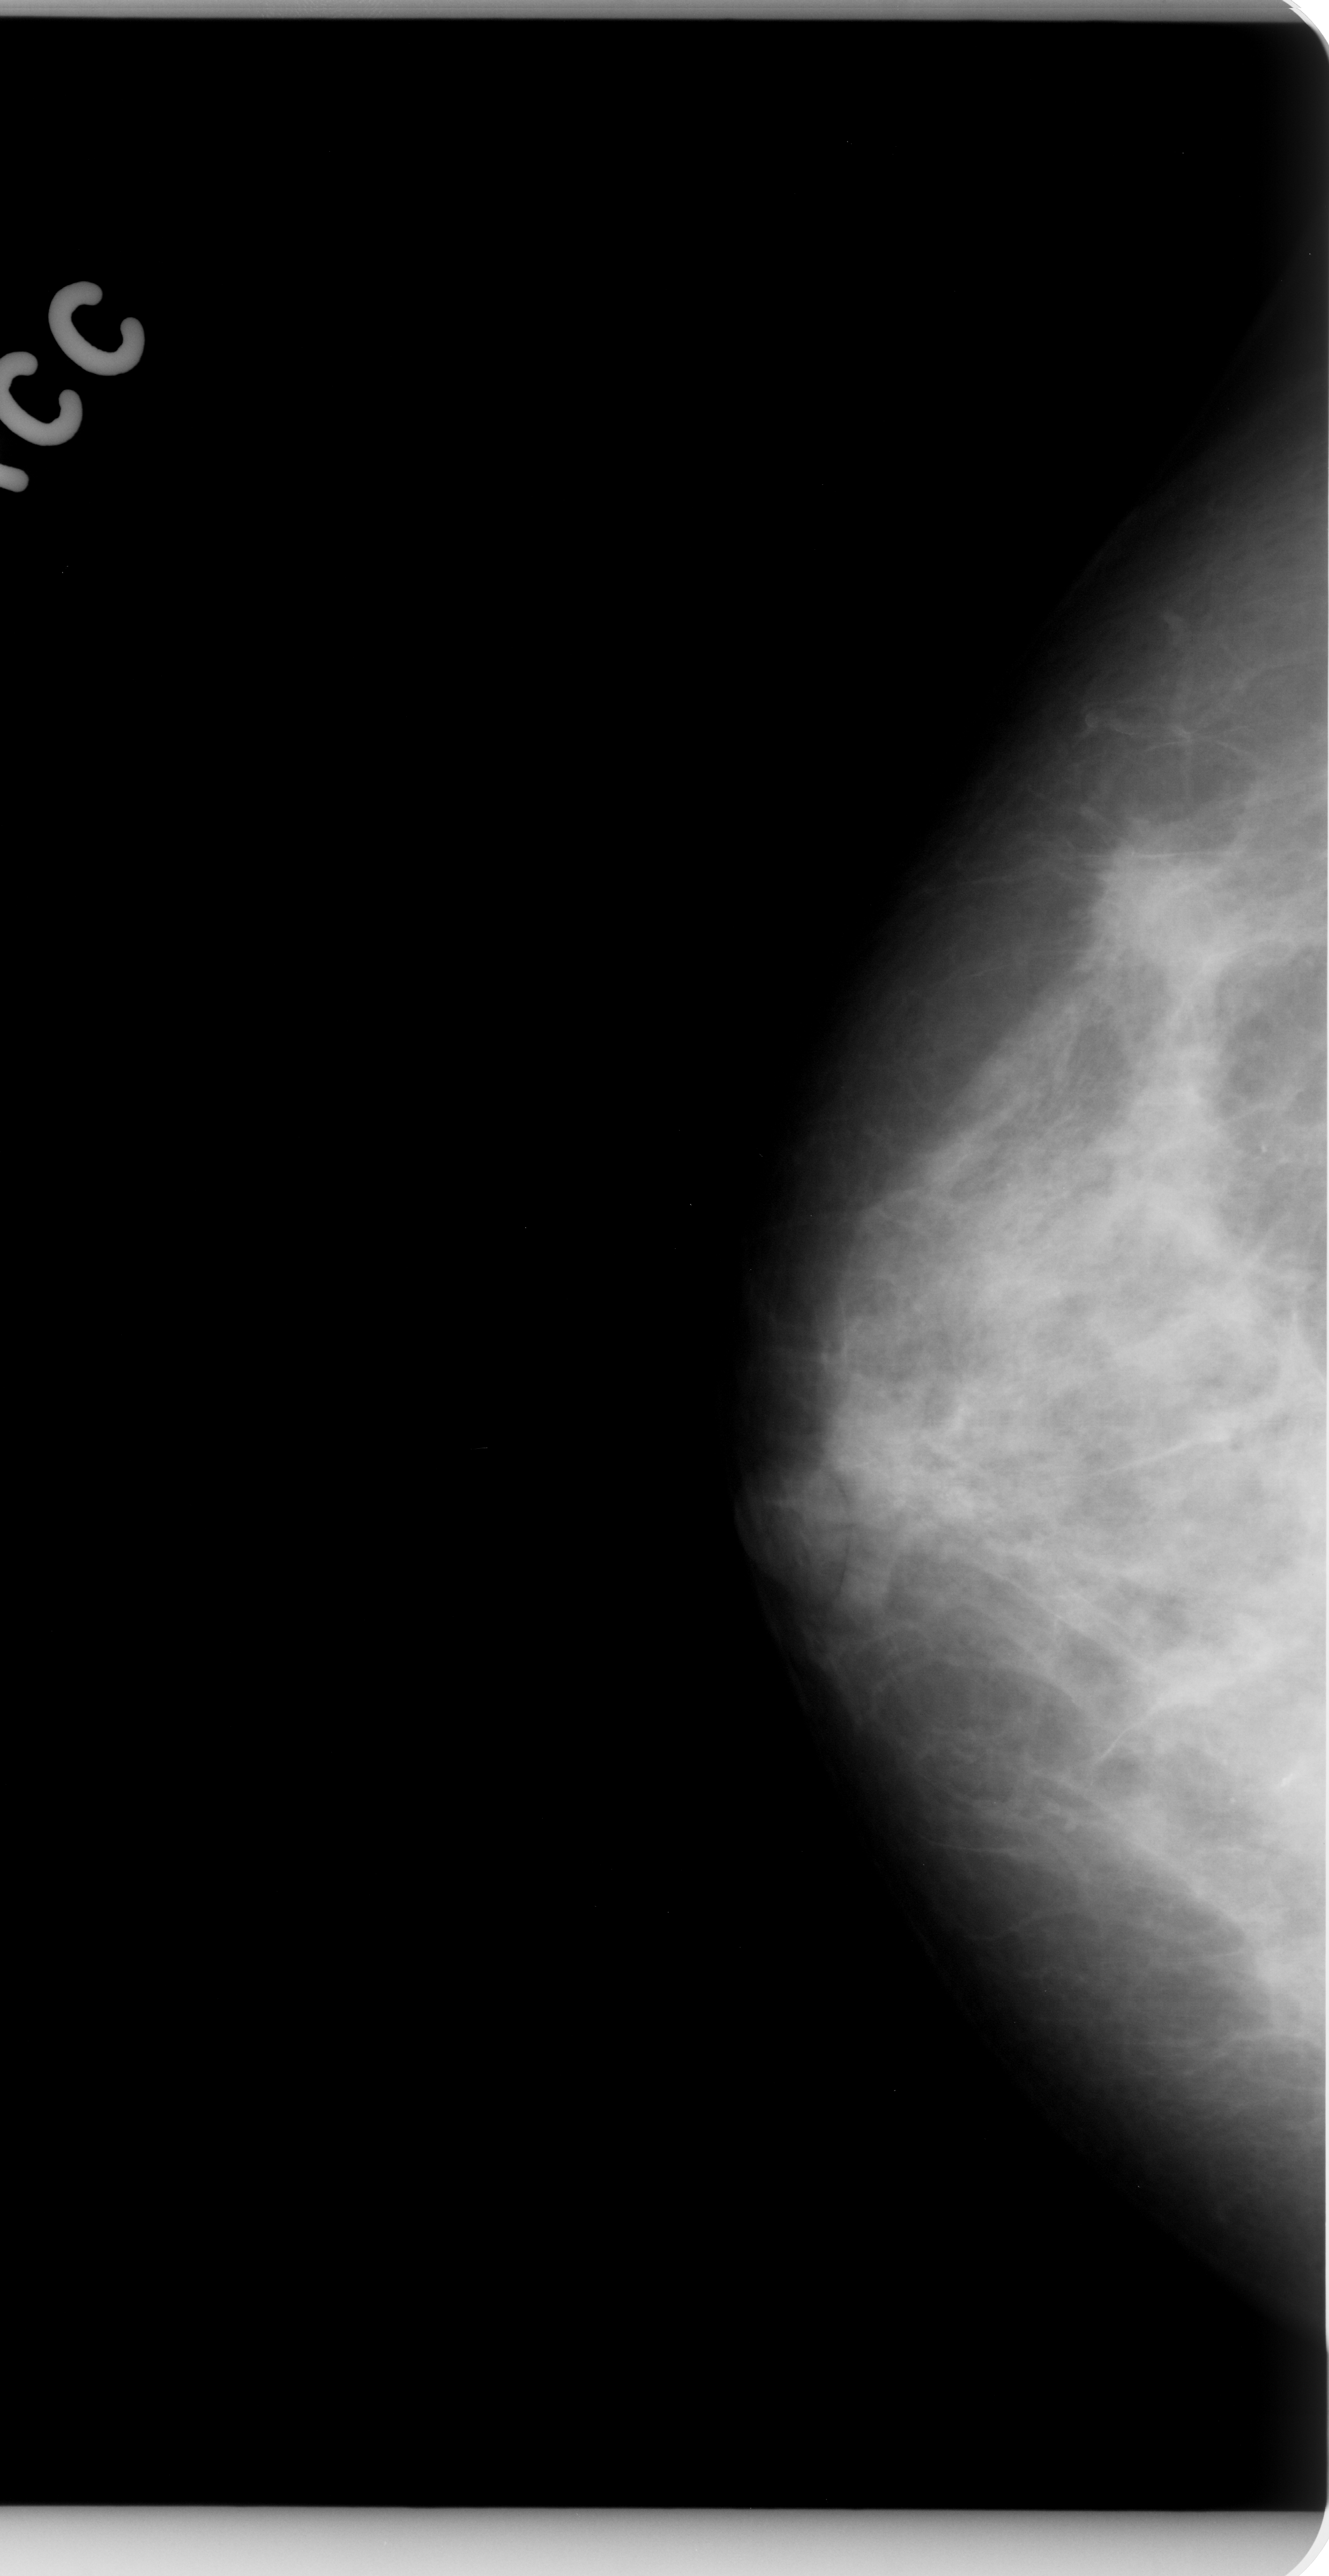
Scanned film-screen mammogram, right breast, craniocaudal (CC) view, breast composition: heterogeneously dense (BI-RADS density category 3 of 4).
- Mass, shape irregular, margins ill defined; BI-RADS assessment category 4; subtlety rating 4 on a 1 (subtle) to 5 (obvious) scale; pathology (as recorded): malignant.